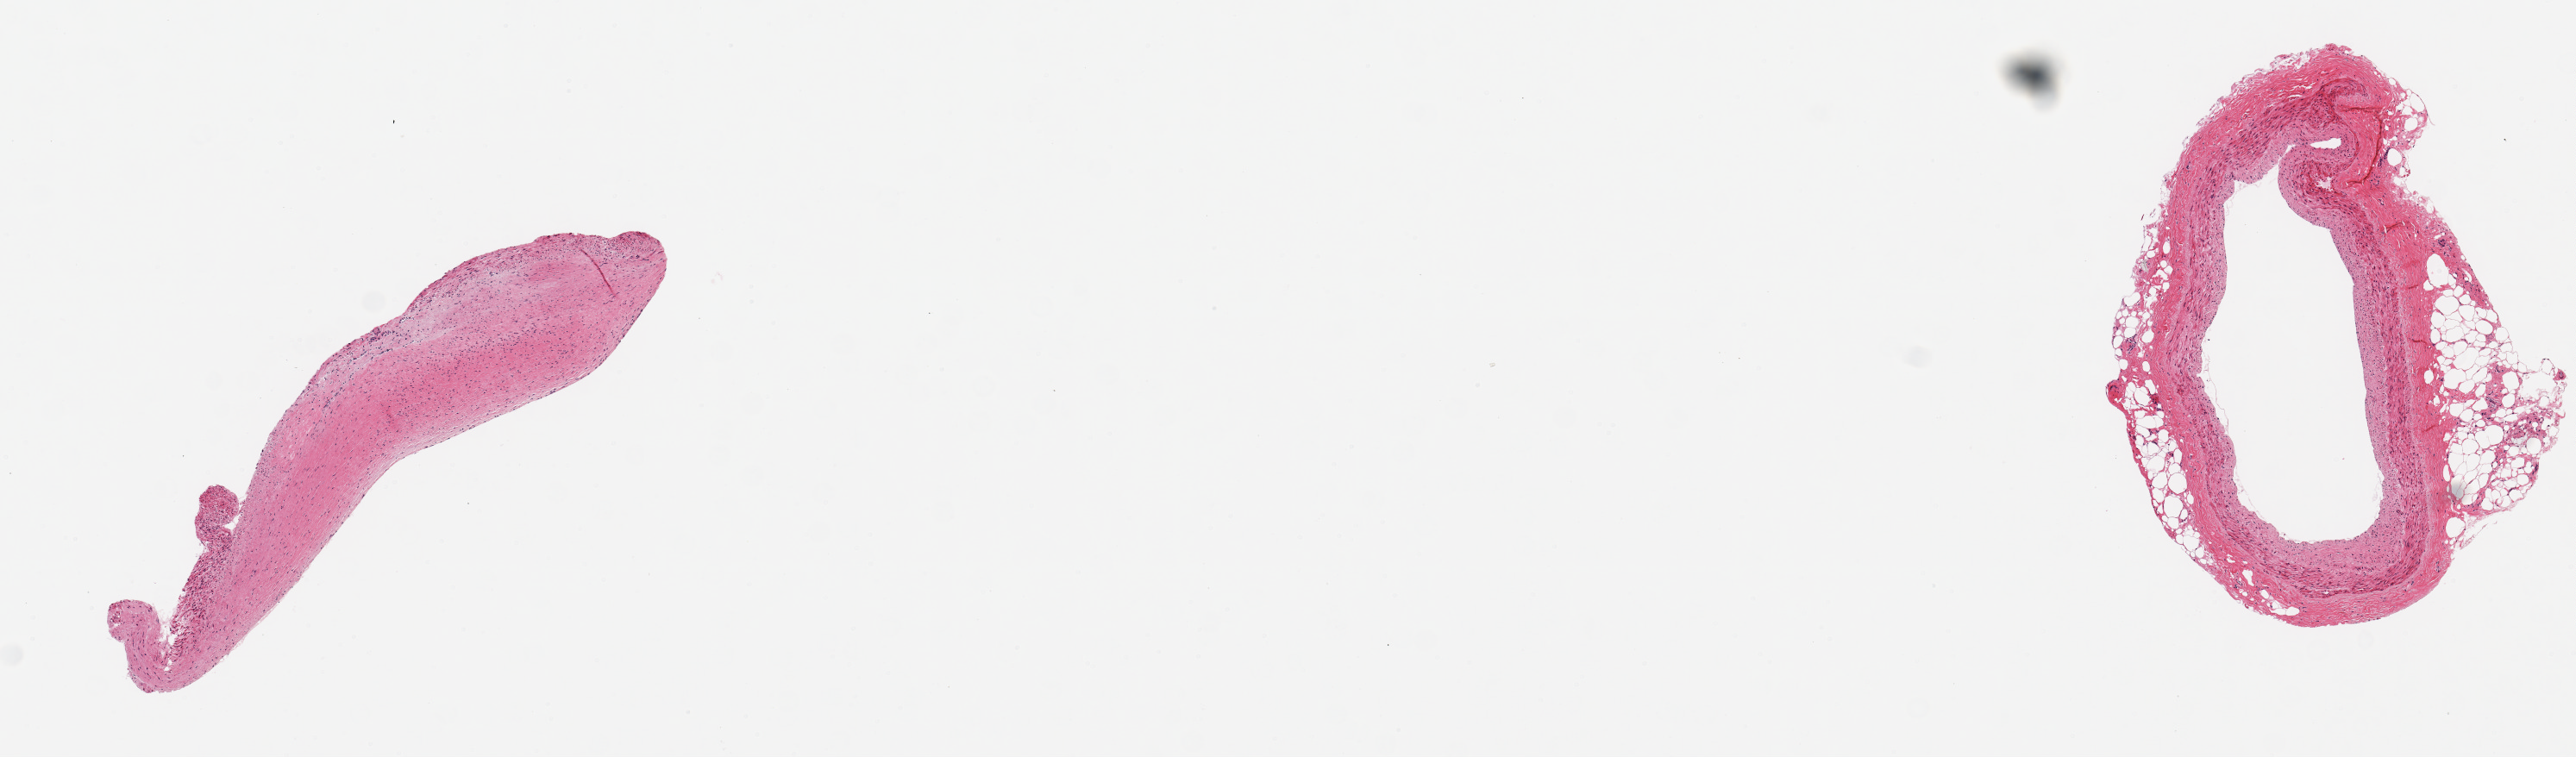
Digitized haematoxylin and eosin-stained section, a low-resolution overview of the entire scanned area, about 11.8 x 3.5 mm. PAXgene-fixed paraffin-embedded (PFPE) section. Target tissue: coronary artery. Donor tissue sample. Female donor.
Review note (as recorded): 2 pieces, one with ~0.6mm nubbins of adherent fat.